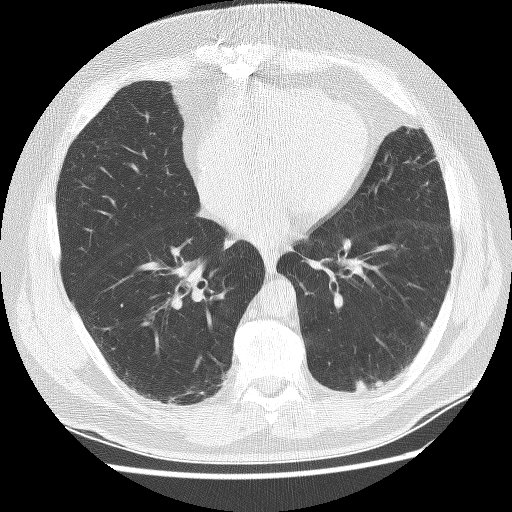
Chest CT (low-dose screening protocol), one axial image, first (baseline) screen, lung window (W 1500 / L -600 HU), 2.5 mm slice thickness, slice 136 of 236 in the series. Male participant, aged 65 years at enrolment. Former smoker at enrolment.
- Lesion marked by an expert reader, bounding box [x1, y1, x2, y2] px = [352, 370, 392, 405].
- Screening reader's record for this exam: no non-calcified nodule ≥4 mm recorded.
- Participant outcome: lung cancer diagnosed 523 days after this screen (after the second annual screen) — squamous cell carcinoma, NOS, left lower lobe, moderately differentiated (G2), stage IA (AJCC 6th edition), 20 mm at pathology.